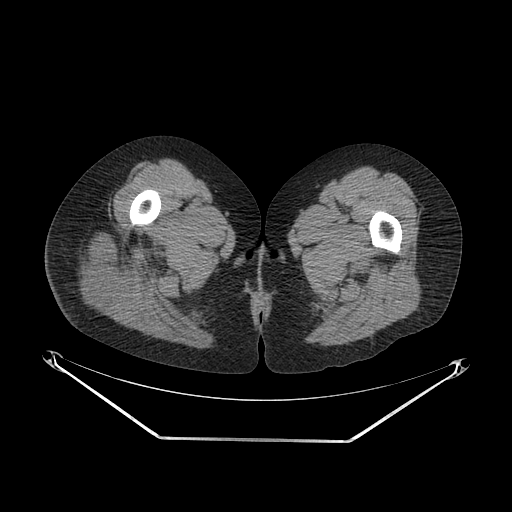
CT of an extremity soft-tissue mass (from a PET/CT study), one axial slice. Position 26 of 267 along the scan axis. Reconstruction kernel SOFT. Soft-tissue window (W 400 / L 40 HU). 3.75 mm slice thickness. 512 × 512 image matrix, field of view 500 × 500 mm. Female patient. Case-level facts recorded for this patient, not image findings: histological type: epithelioid sarcoma with vascular differentiation; site of the primary tumour: right buttock.
Outlined on this slice (expert contour drawn on MRI and transferred to this co-registered scan by the dataset authors):
- gross tumour volume (mass): bounding box (x1, y1, x2, y2) in pixels: (80, 237, 126, 305)